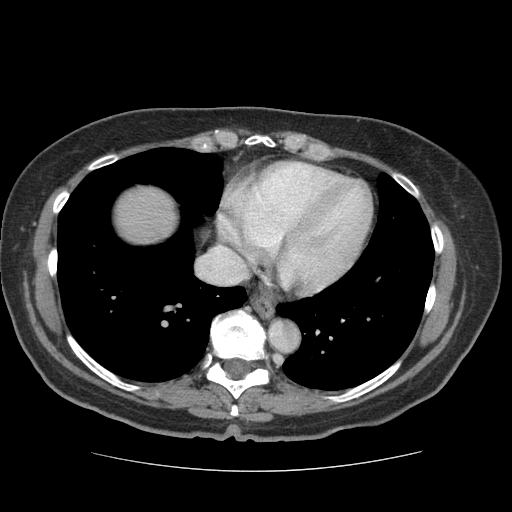
Contrast-enhanced abdominal CT (liver protocol), one axial slice; slice 70 of 75 in the series (ordered by position); 140 kVp; soft-tissue window (W 400 / L 40 HU); 2.5 mm slice thickness; 512 × 512 image matrix. From the clinical record (not read from this slice): diagnosis: hepatocellular carcinoma (patient treated with transarterial chemoembolisation; whether this scan precedes or follows treatment is not stated here); TNM stage (as recorded): Stage-I; Child-Pugh class: A; tumour differentiation: moderately differentiated; tumour nodularity: uninodular.
Outlined on this slice (semi-automatic segmentation, software-assisted and operator-edited):
- liver parenchyma outside the tumour (the mass and vessels are separate outlines, so this box may not span the whole liver): box from (x=114, y=186) to (x=176, y=244) px